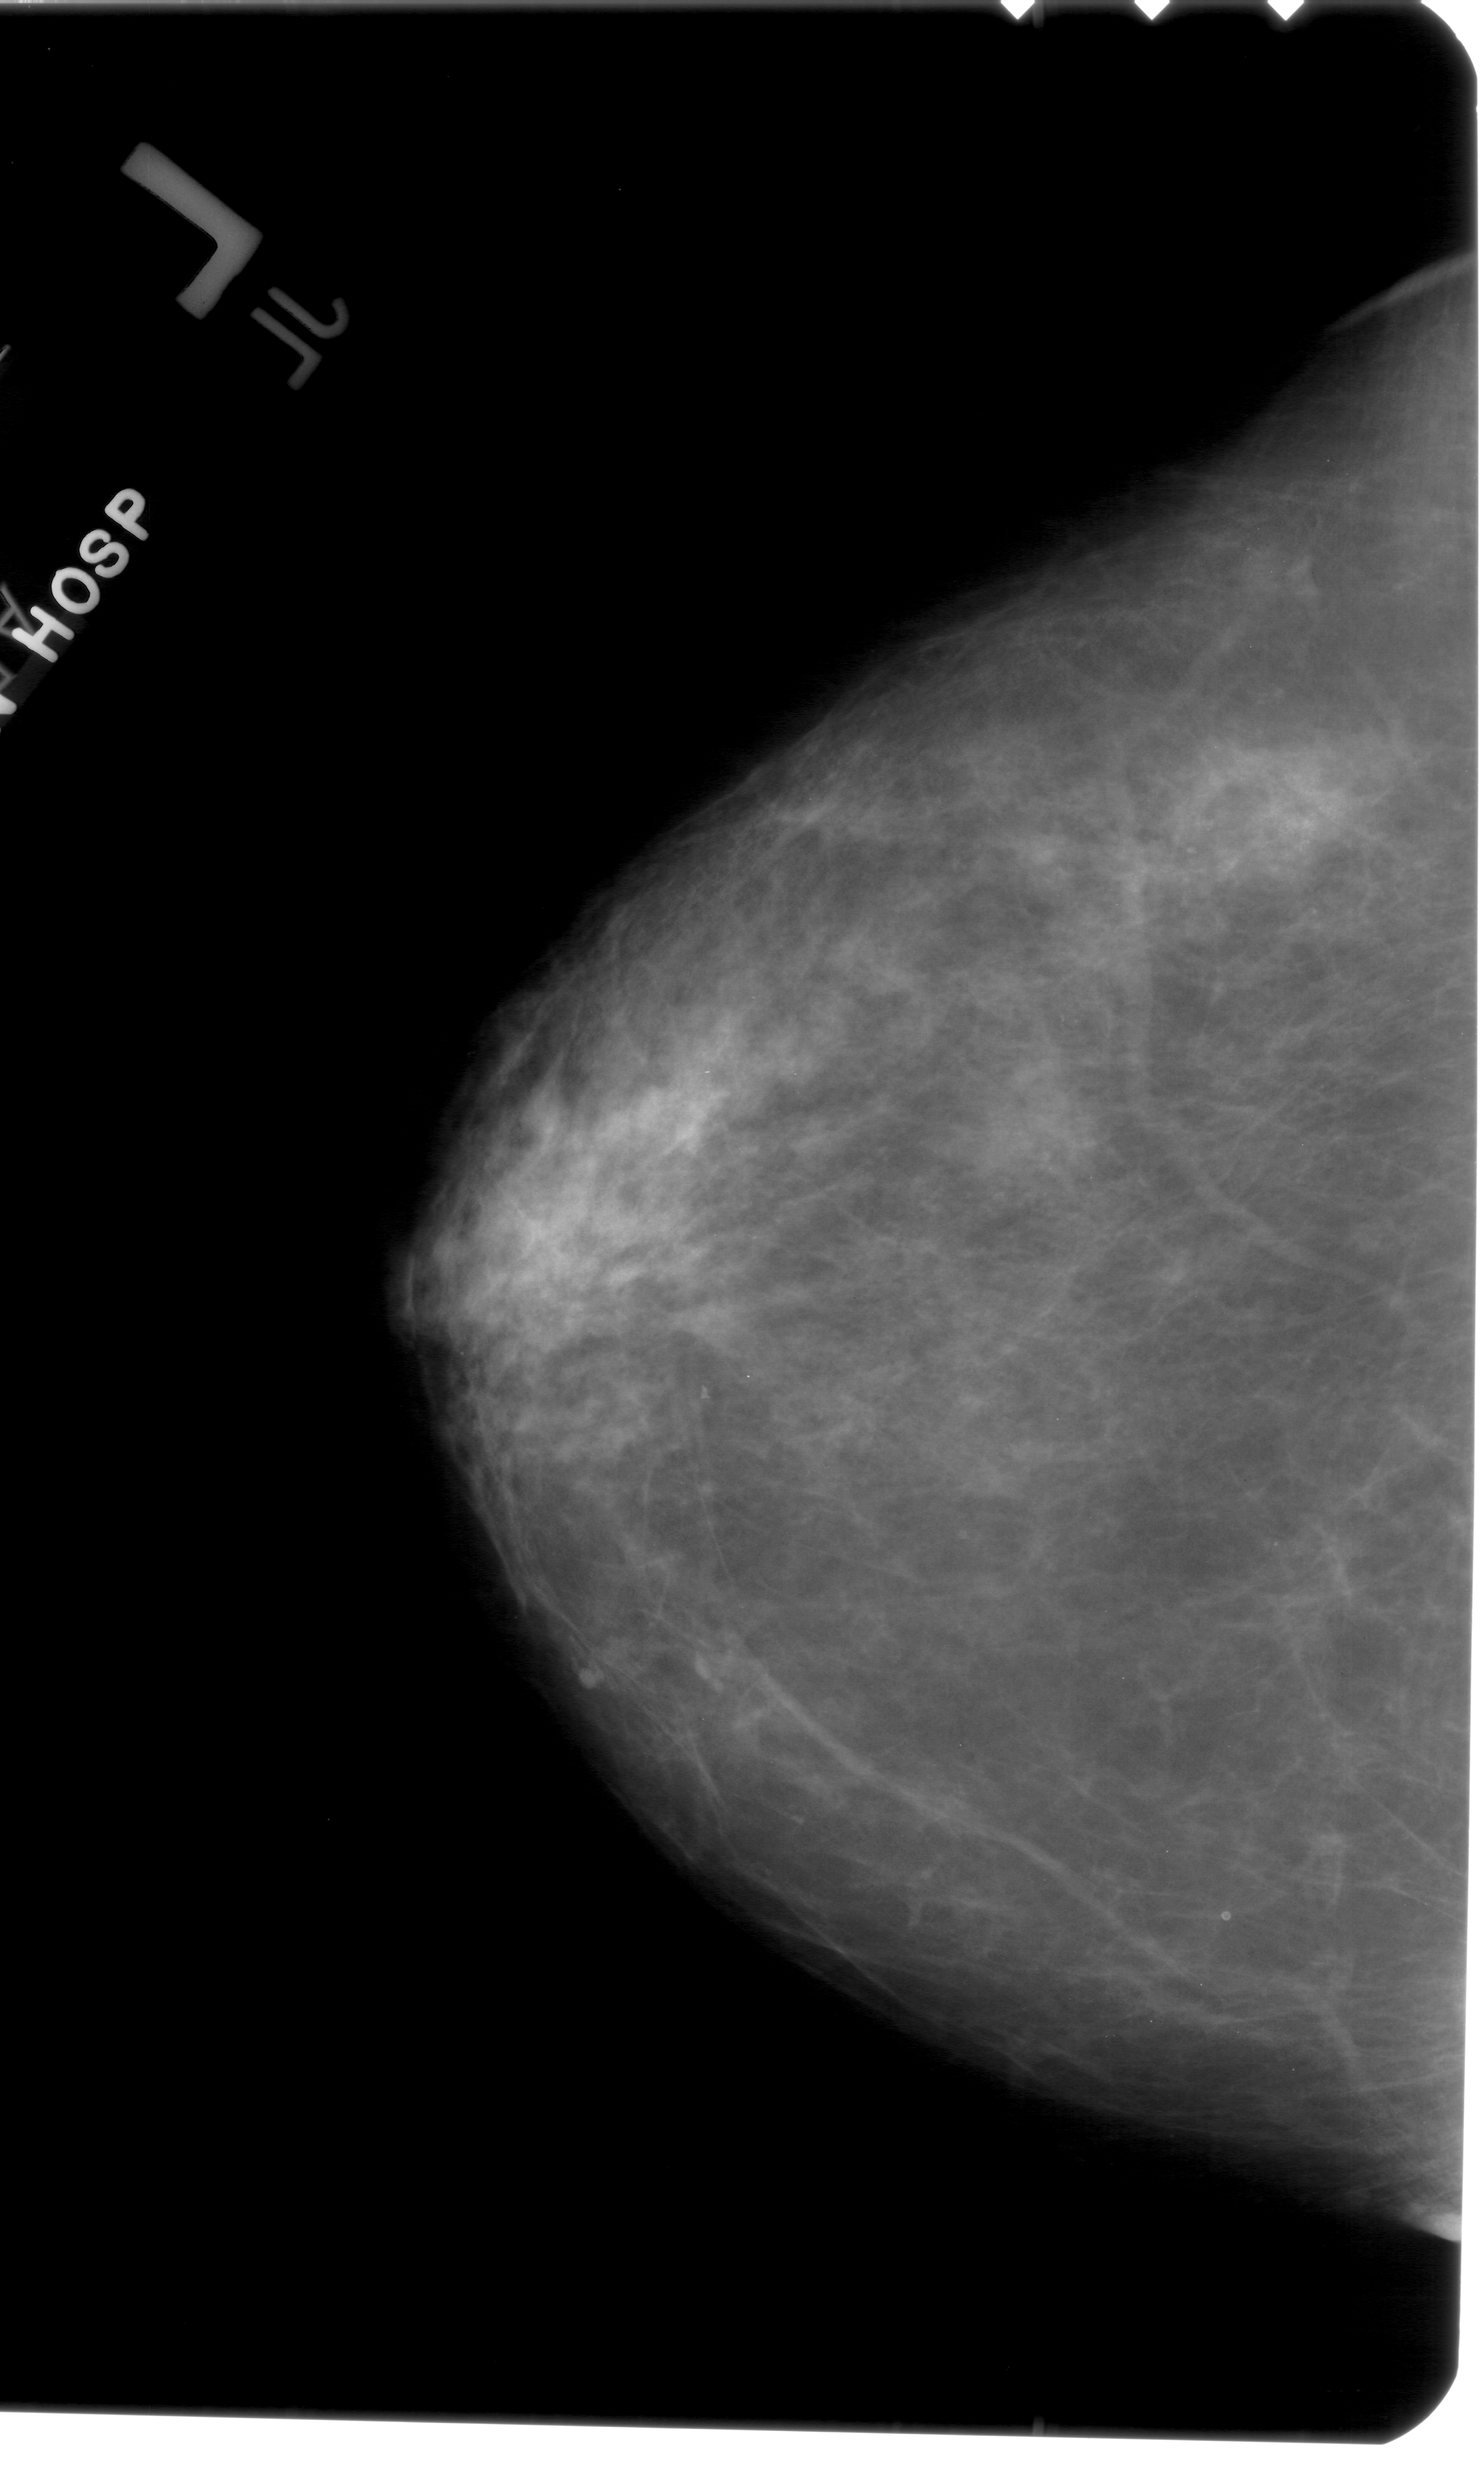
Scanned film-screen mammogram, left breast, CC view.
- Calcifications, morphology amorphous, distribution clustered; BI-RADS assessment category 4; pathology result (as recorded, not read from the image): benign.